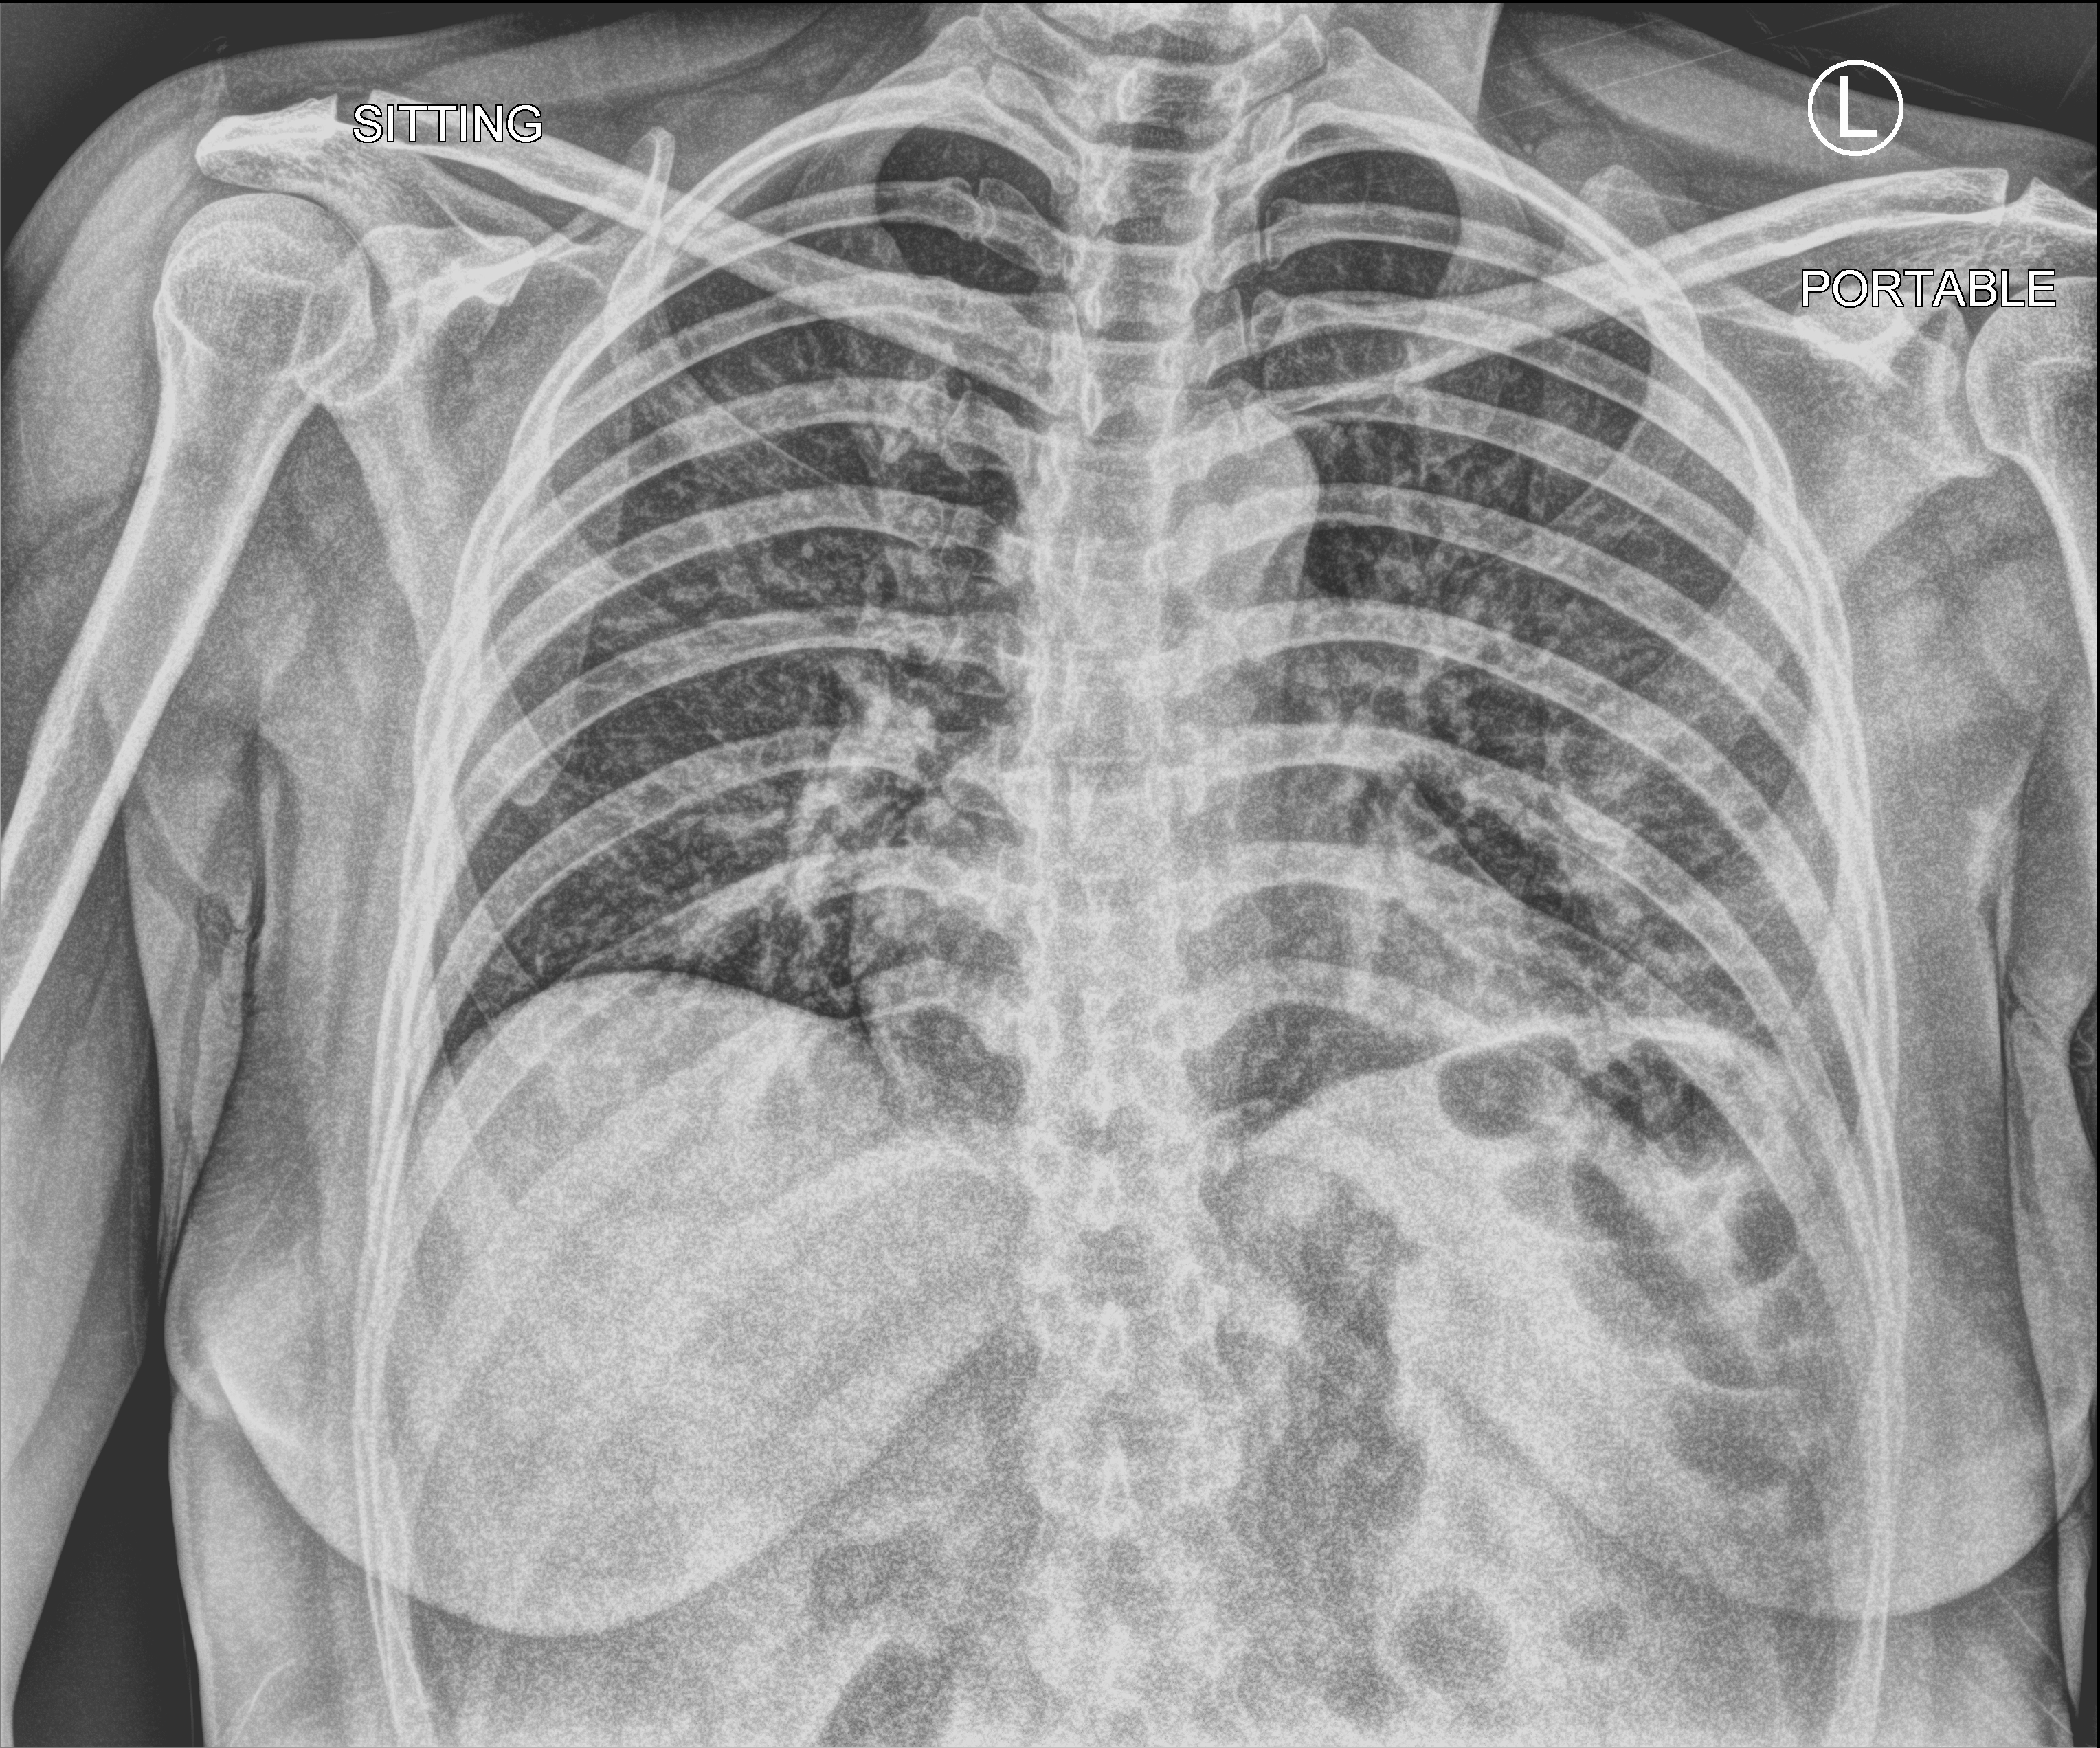
Chest X-ray (portable); anteroposterior (AP) projection. Female patient hospitalised with COVID-19, age 18–59 years.
From the hospital-stay record, not from the radiograph (when in the stay this image was taken is not recorded): length of hospital stay: 1 day; admitted to intensive care during this hospital stay: no.